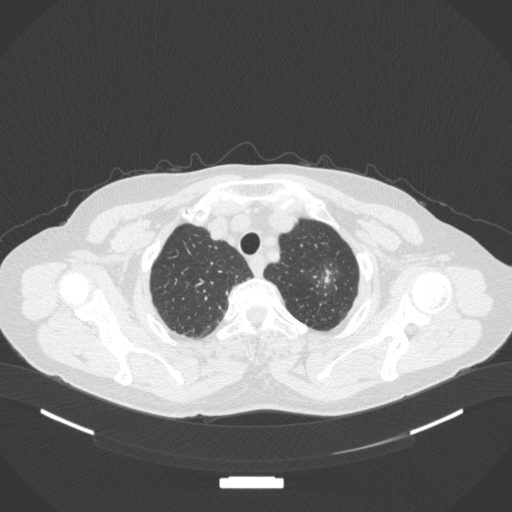
Chest CT, one axial slice; slice 315 of 369 in the series (ordered by position); reconstruction kernel B31f; 120 kVp; lung window (W 1500 / L -600 HU); 1 mm slice thickness; 512 × 512 image matrix, field of view 400 × 400 mm. Patient: female, 64 years. From the clinical record (not read from this slice): clinical TNM (as recorded): T1c N0 M0.
Outlined on this slice (rectangle marked by the reading radiologist):
- lung tumour (recorded histology: adenocarcinoma): box from (x=303, y=258) to (x=342, y=306) px